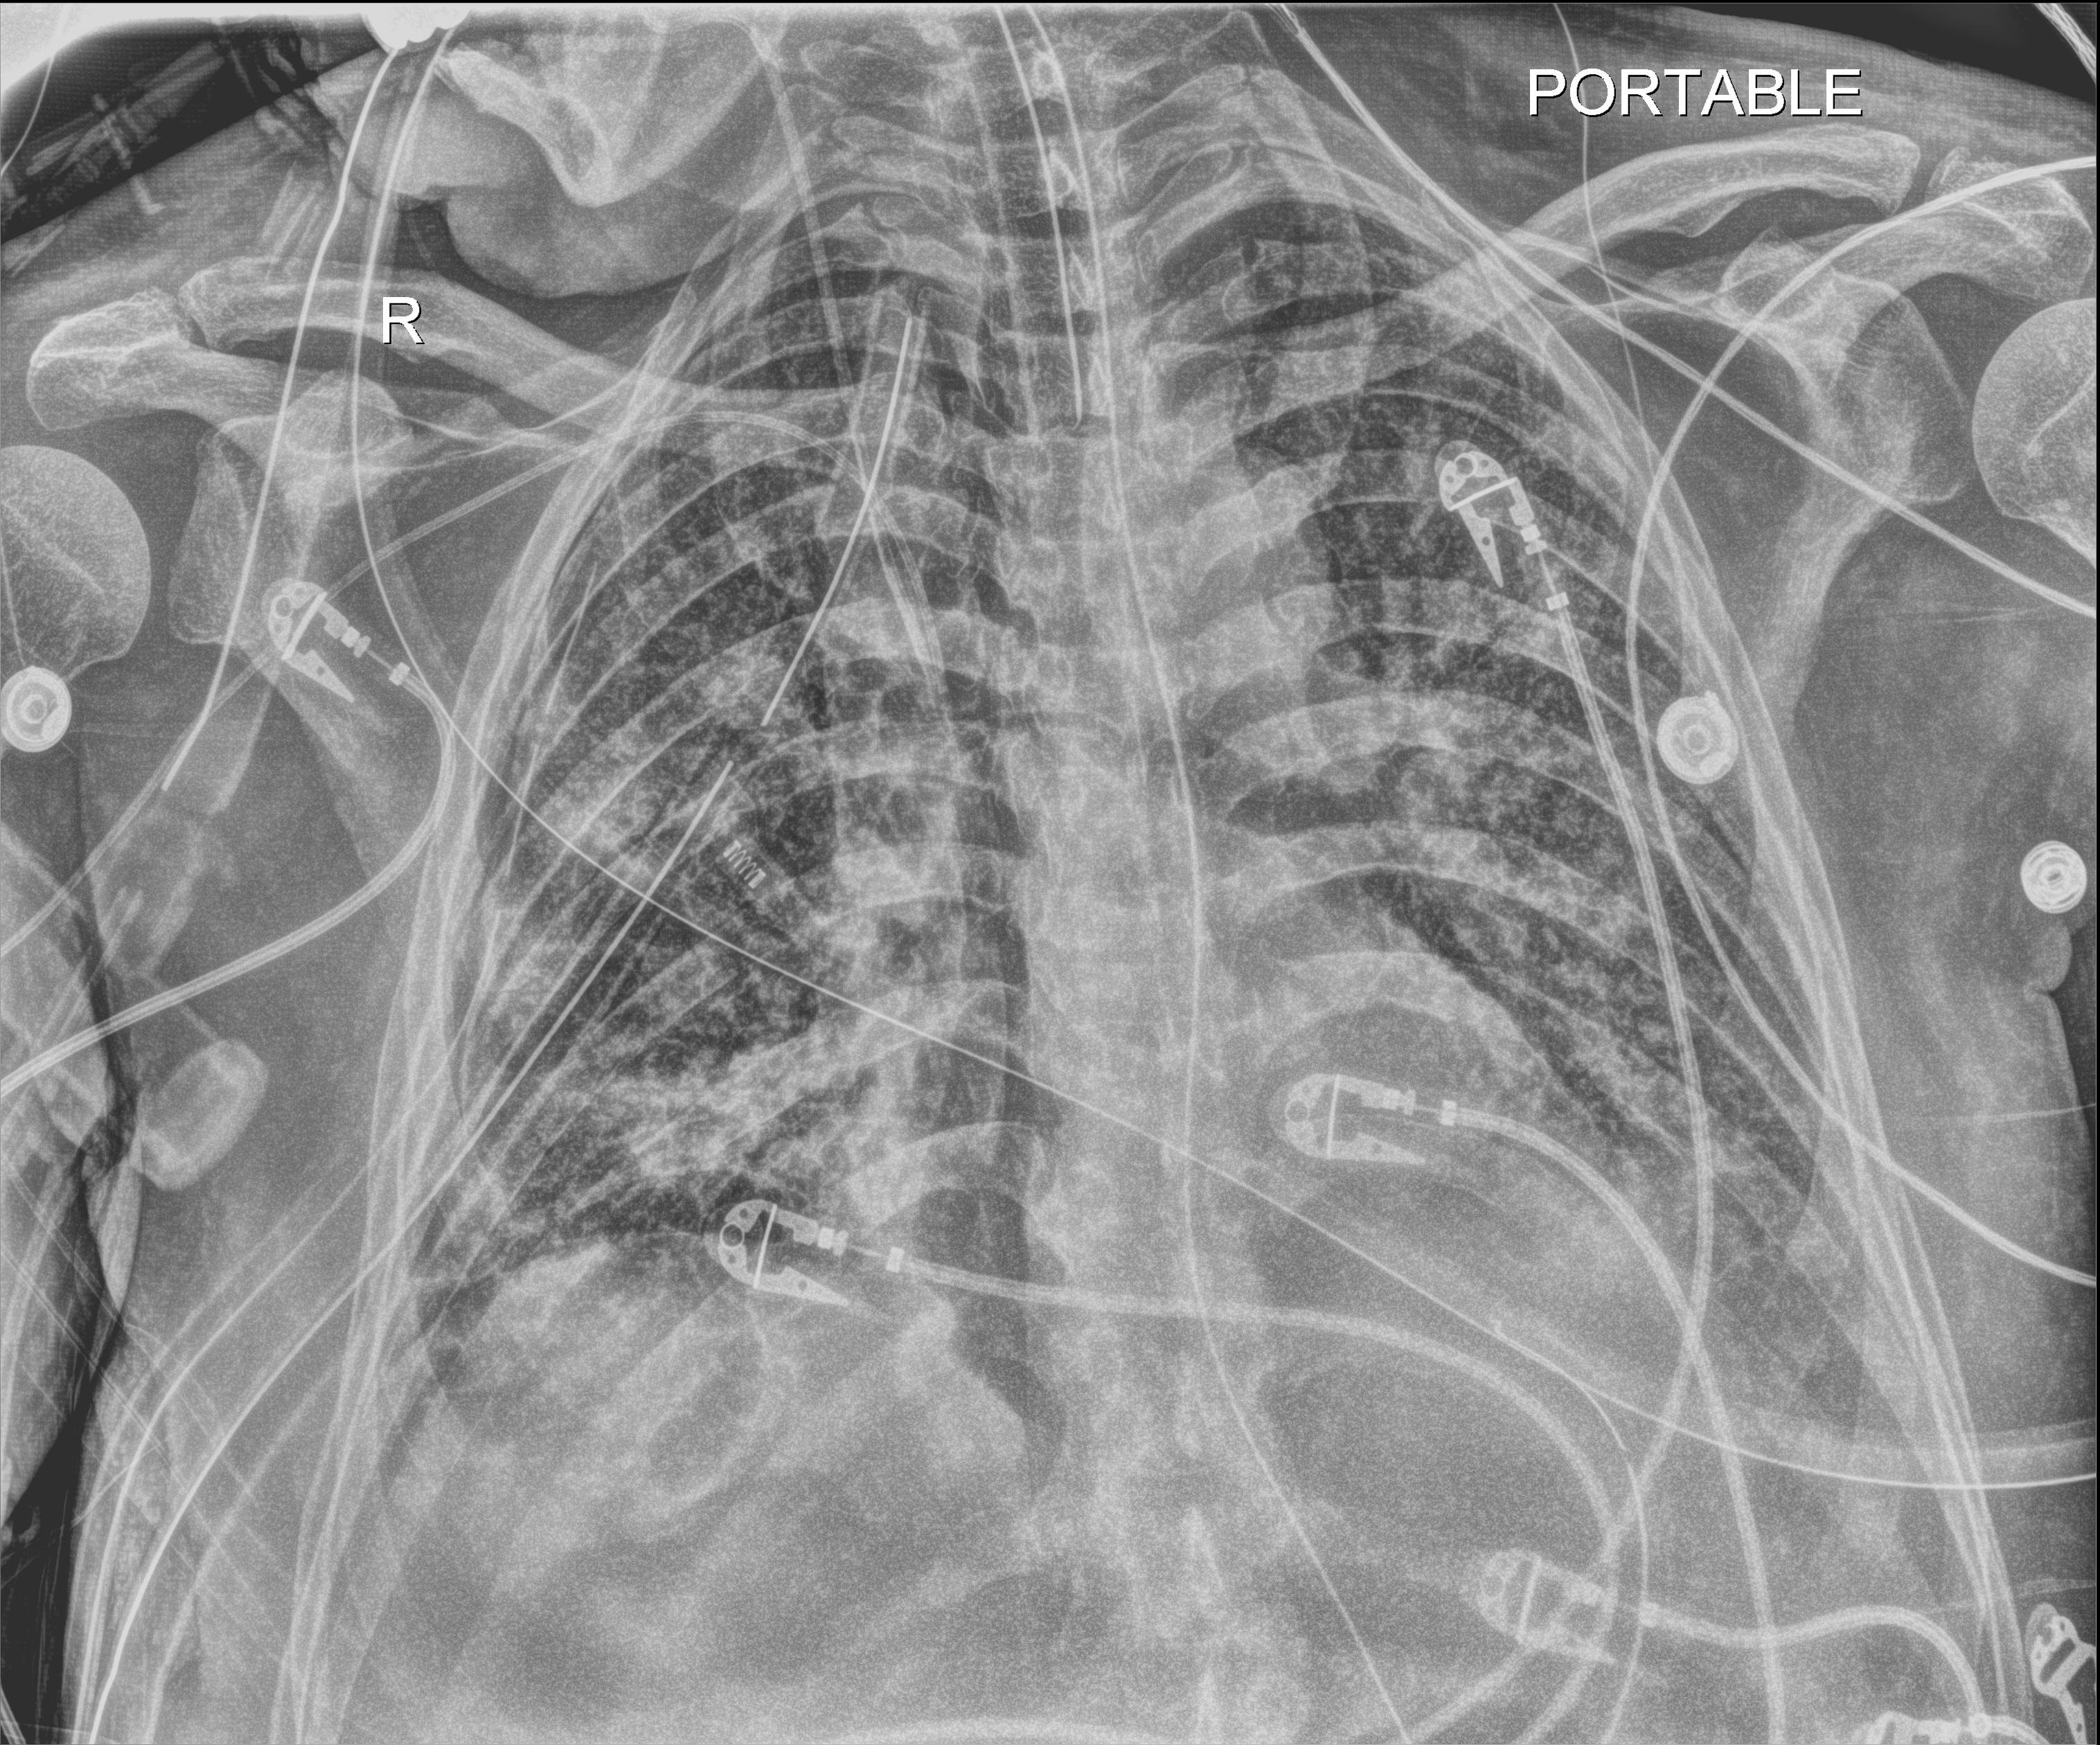
Portable chest radiograph; anteroposterior (AP) projection. Male patient hospitalised with COVID-19, age 60–74 years.
Hospital-stay facts (about this admission, not read from this image; timing relative to this image not recorded): mechanically ventilated during this hospital stay: yes; admitted to intensive care during this hospital stay: yes.